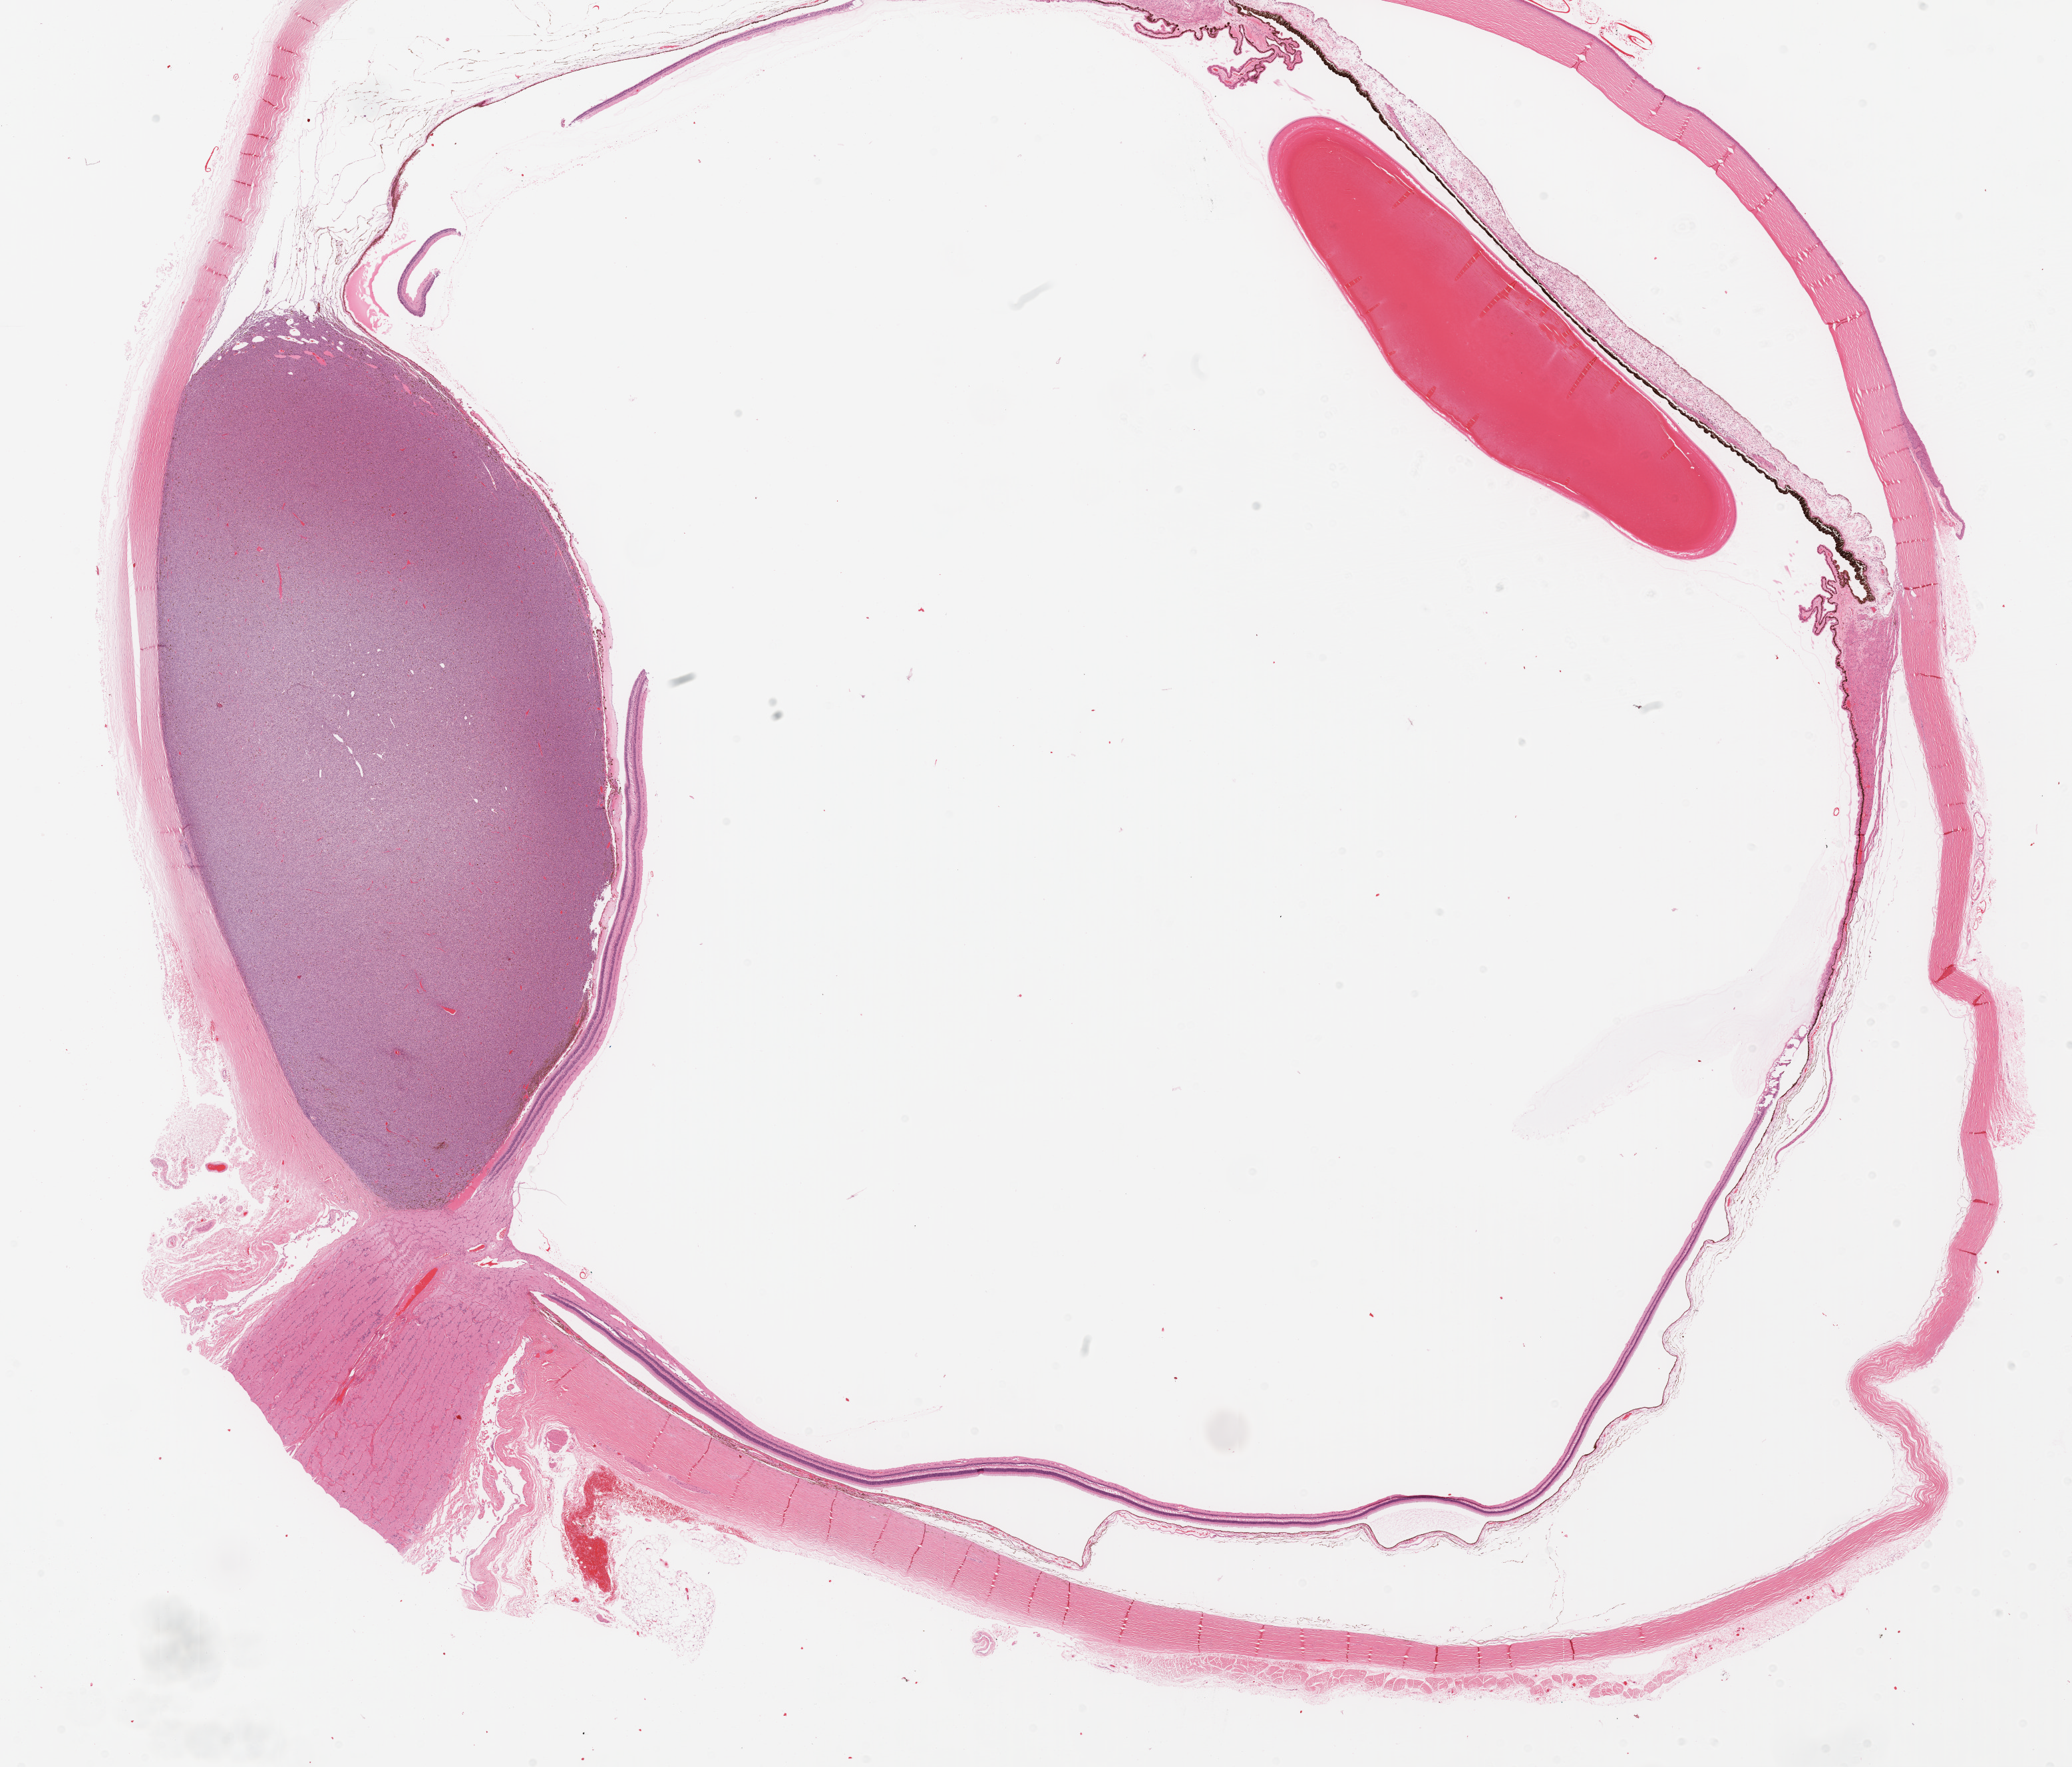
H&E-stained whole-slide image — shown as a low-resolution overview of the whole scanned area (about 25.1 x 21.4 mm). Formalin-fixed paraffin-embedded (FFPE) diagnostic section. Sample: primary tumour, uvea. Patient: male, age at initial diagnosis 40 years.
Laterality: right. Pathologic diagnosis: Spindle cell melanoma, NOS (choroid). AJCC pathologic stage: IIA (7th edition).